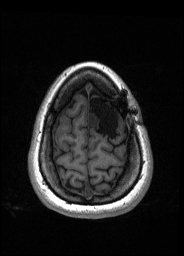
Pre-operative brain MRI before brain-tumour surgery, one axial slice. Slice 38 of 176 in the series (ordered by position). T1-weighted post-contrast. 1 mm slice thickness. 184 × 256 image matrix, field of view 180 × 250 mm. Case-level facts recorded for this patient, not image findings: histopathology: Oligodendroglioma; WHO grade: 2; IDH mutation: yes; tumour location: Left Frontal.
Annotated regions visible in this slice (manually delineated by an expert):
- tumour: bounding box [x1, y1, x2, y2] px = [88, 112, 100, 128]